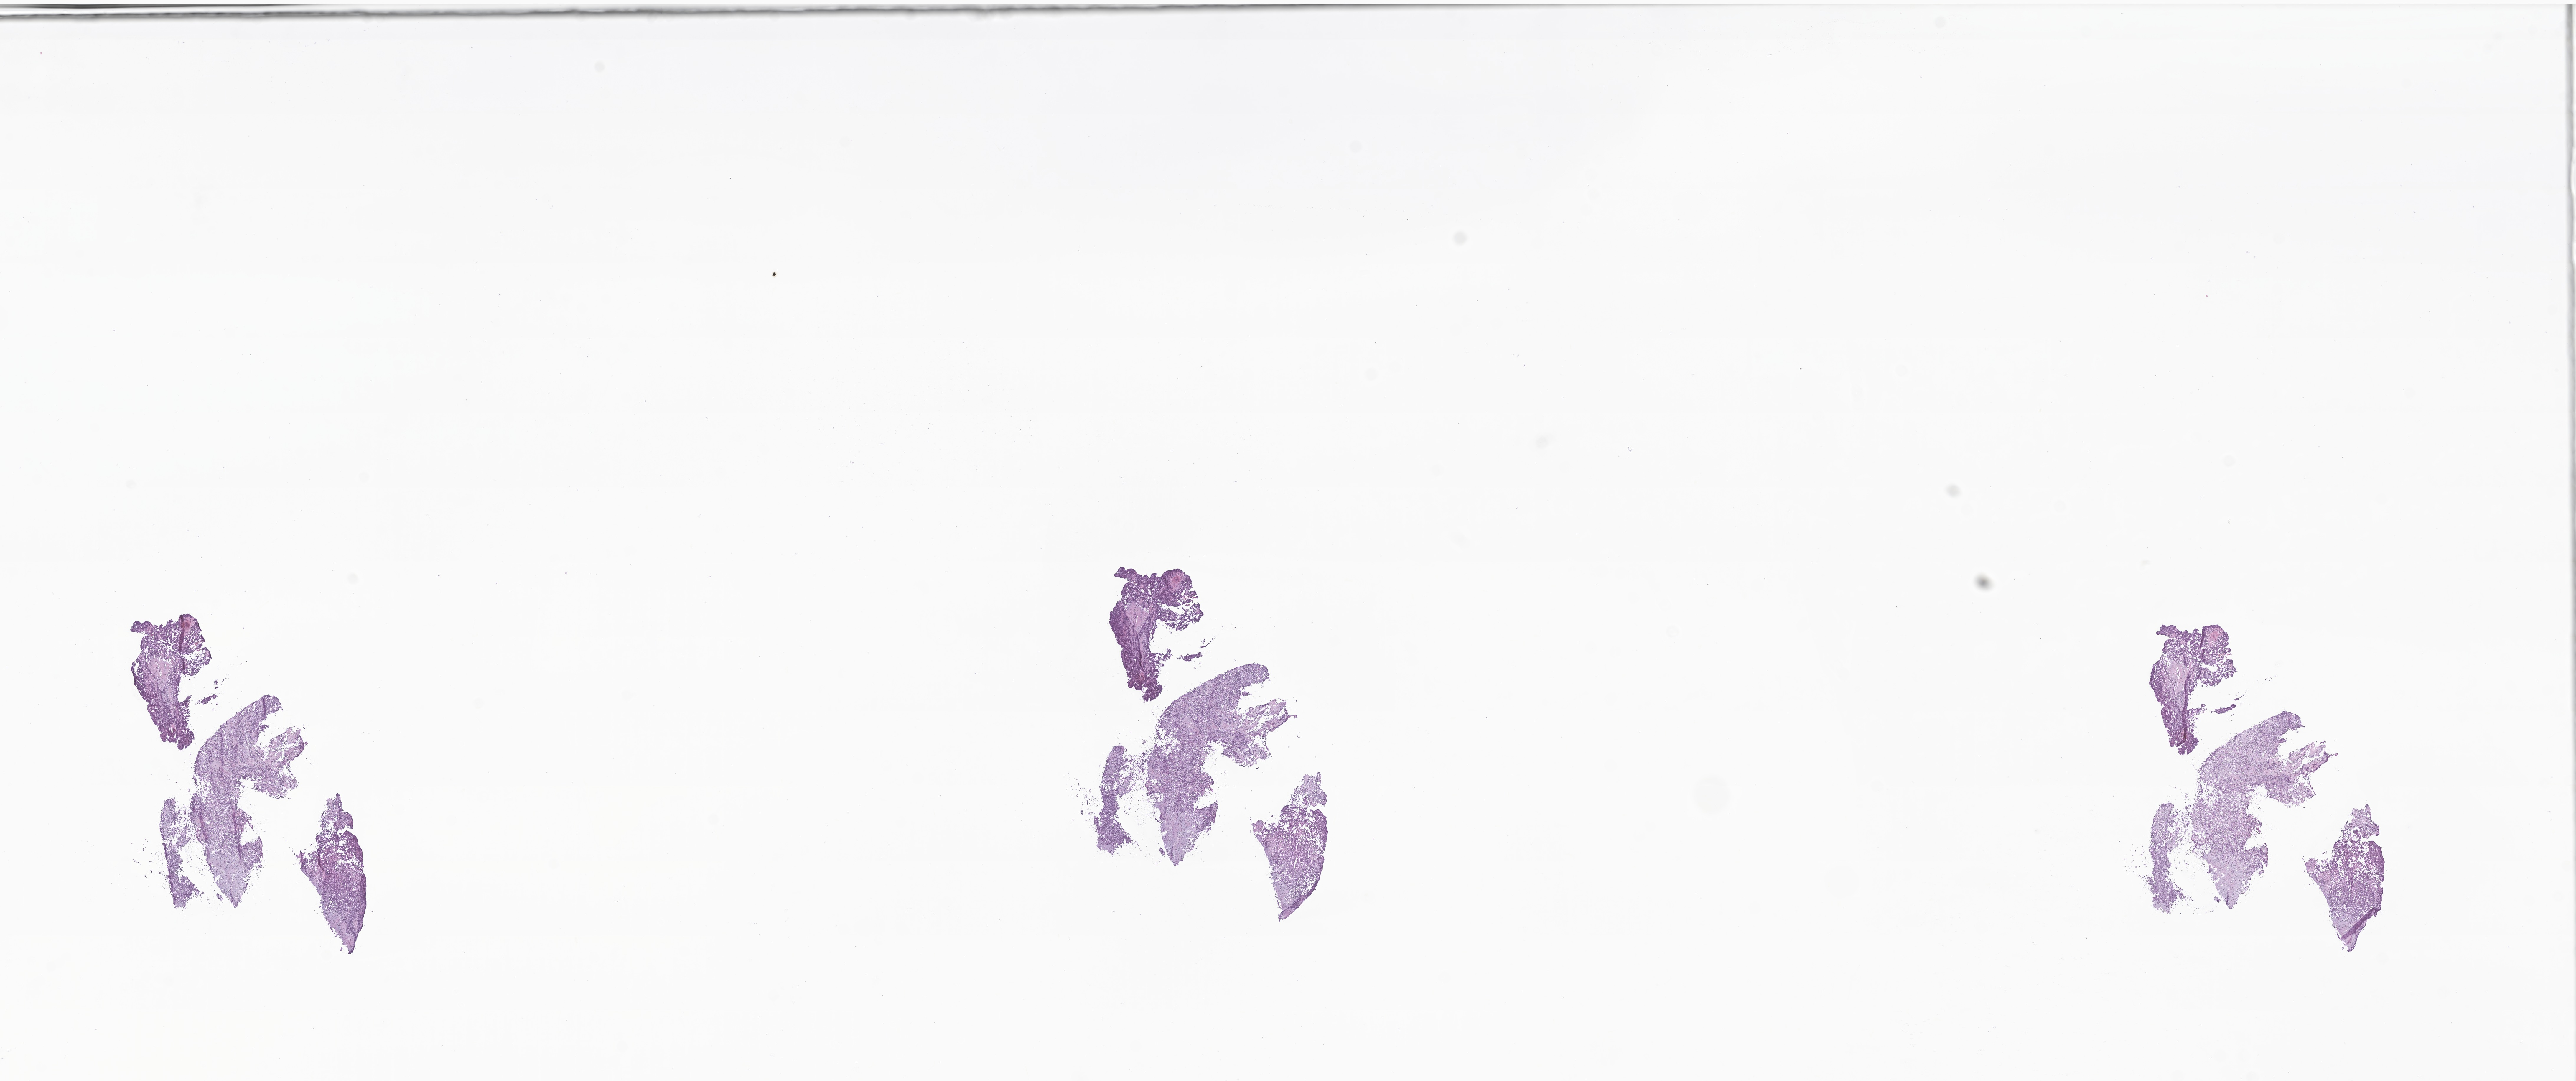
Whole-slide image, haematoxylin and eosin stain of tumor tissue from the frontal lobe, shown as a low-resolution overview of the whole scanned area (about 36.8 x 15.5 mm). Cryosection (OCT / tissue freezing medium). Patient female; age 193 months (16 years 1 month).
- diagnosis: Mesenchymal chondrosarcoma